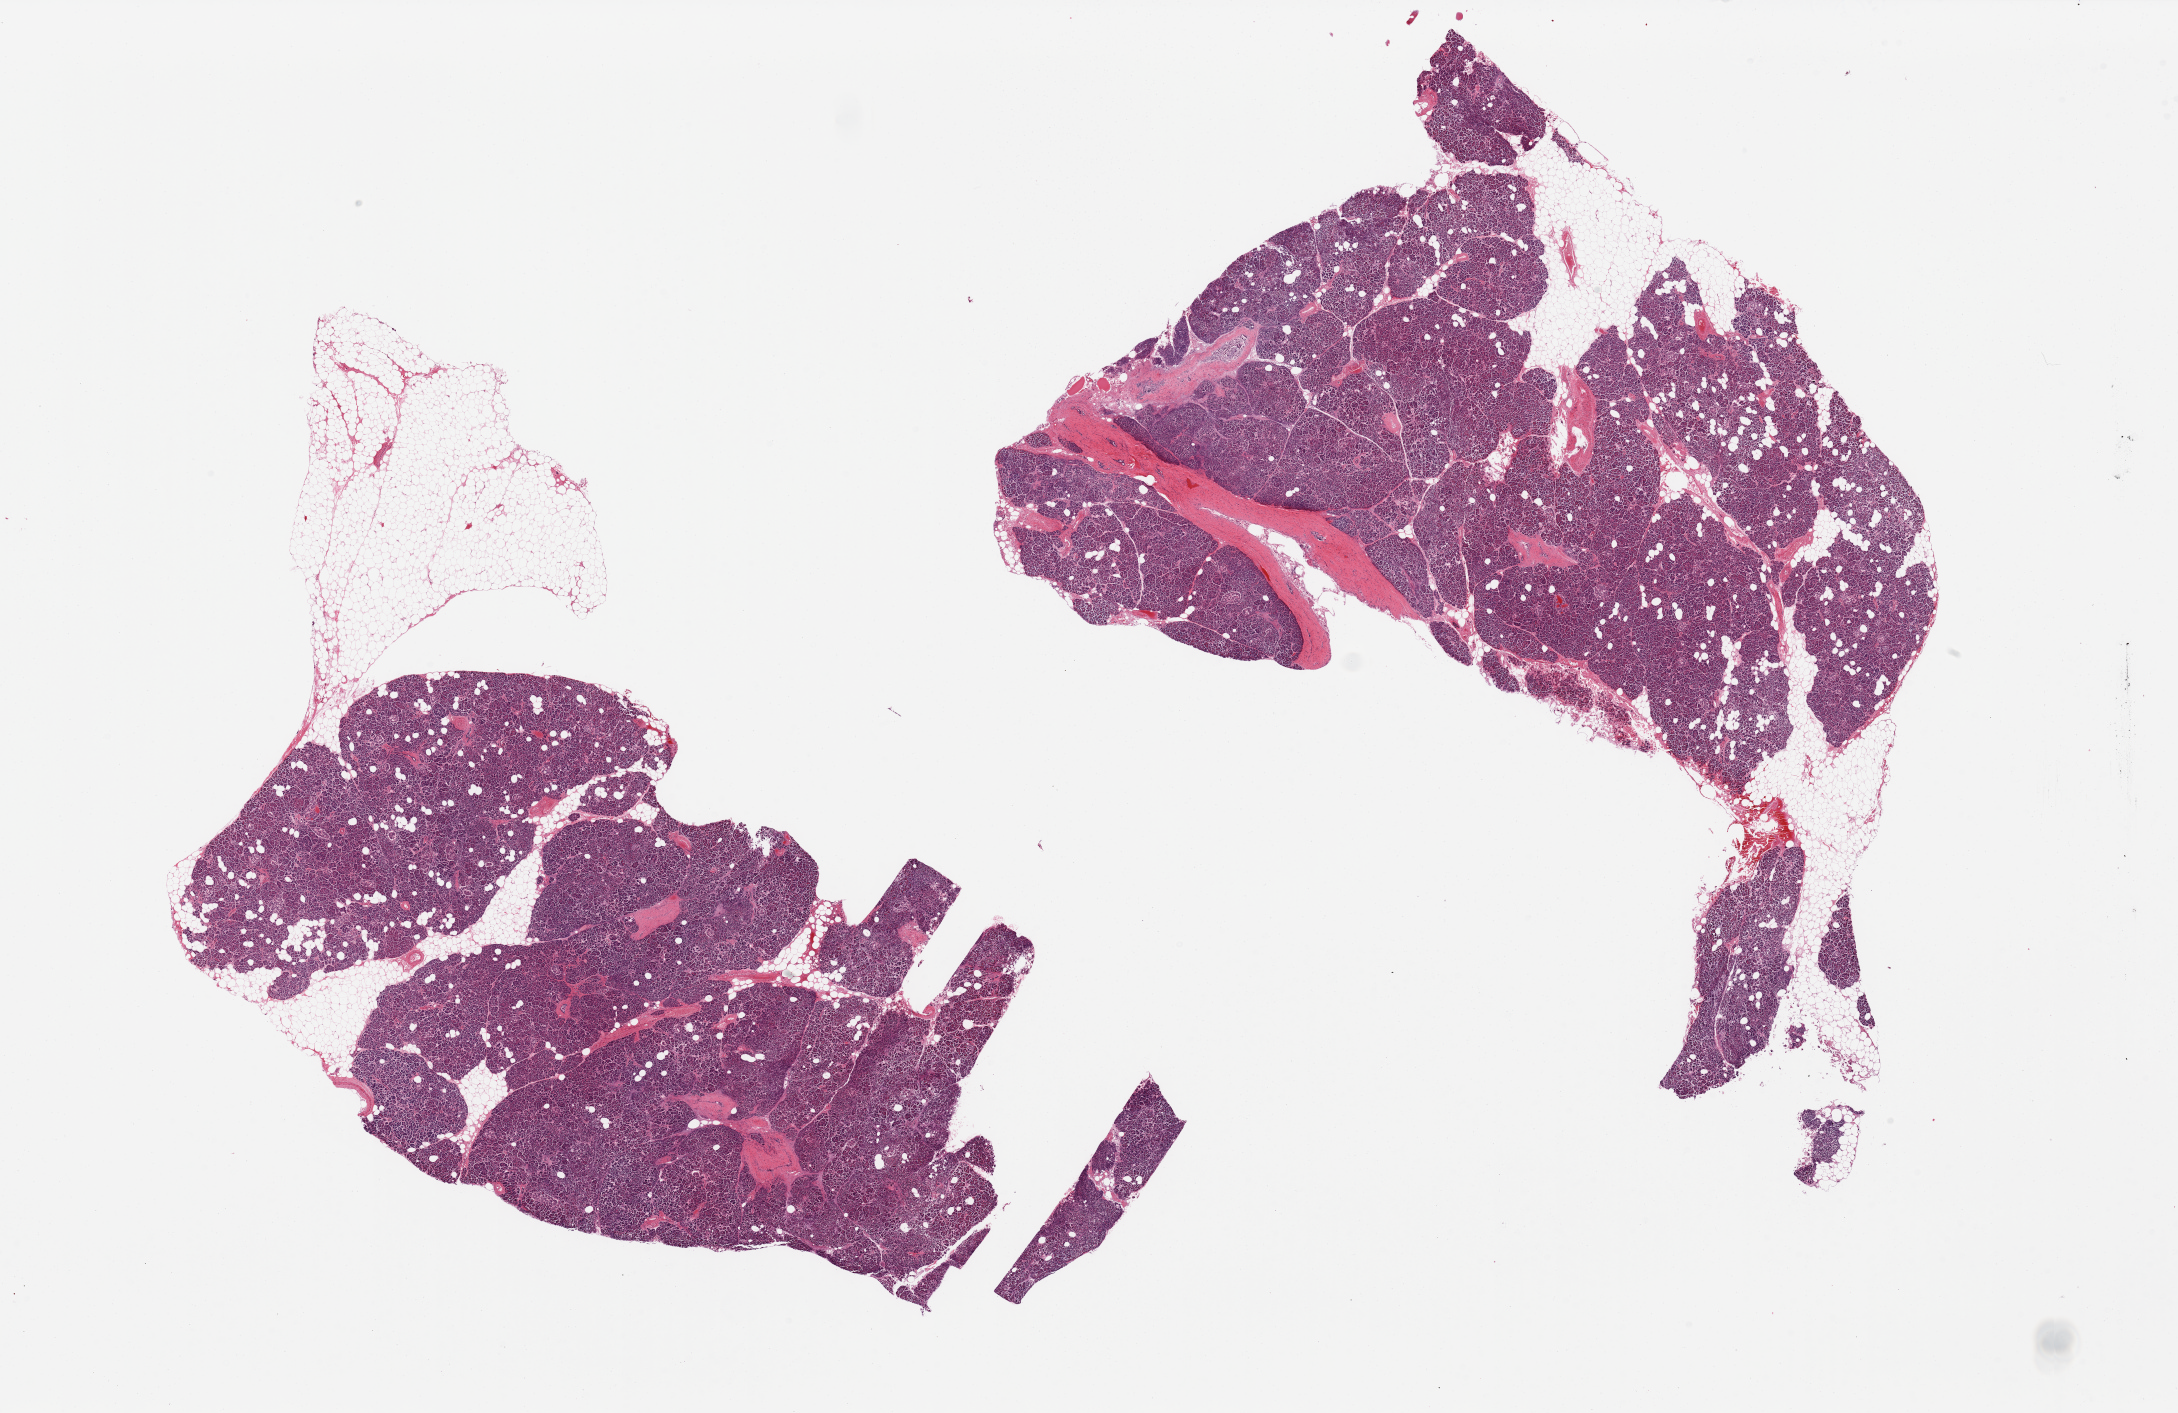
Digitized hematoxylin and eosin (H&E)-stained section, brightfield, a low-resolution overview of the entire scanned area, about 34.5 x 22.4 mm, PAXgene-fixed paraffin-embedded (PFPE) section, section of pancreas (target tissue), donor tissue sample.
* reviewer comment on this tissue sample: 2 pieces, attachment of adipose tissue (10 and 20%), moderate to focally severe autolysis